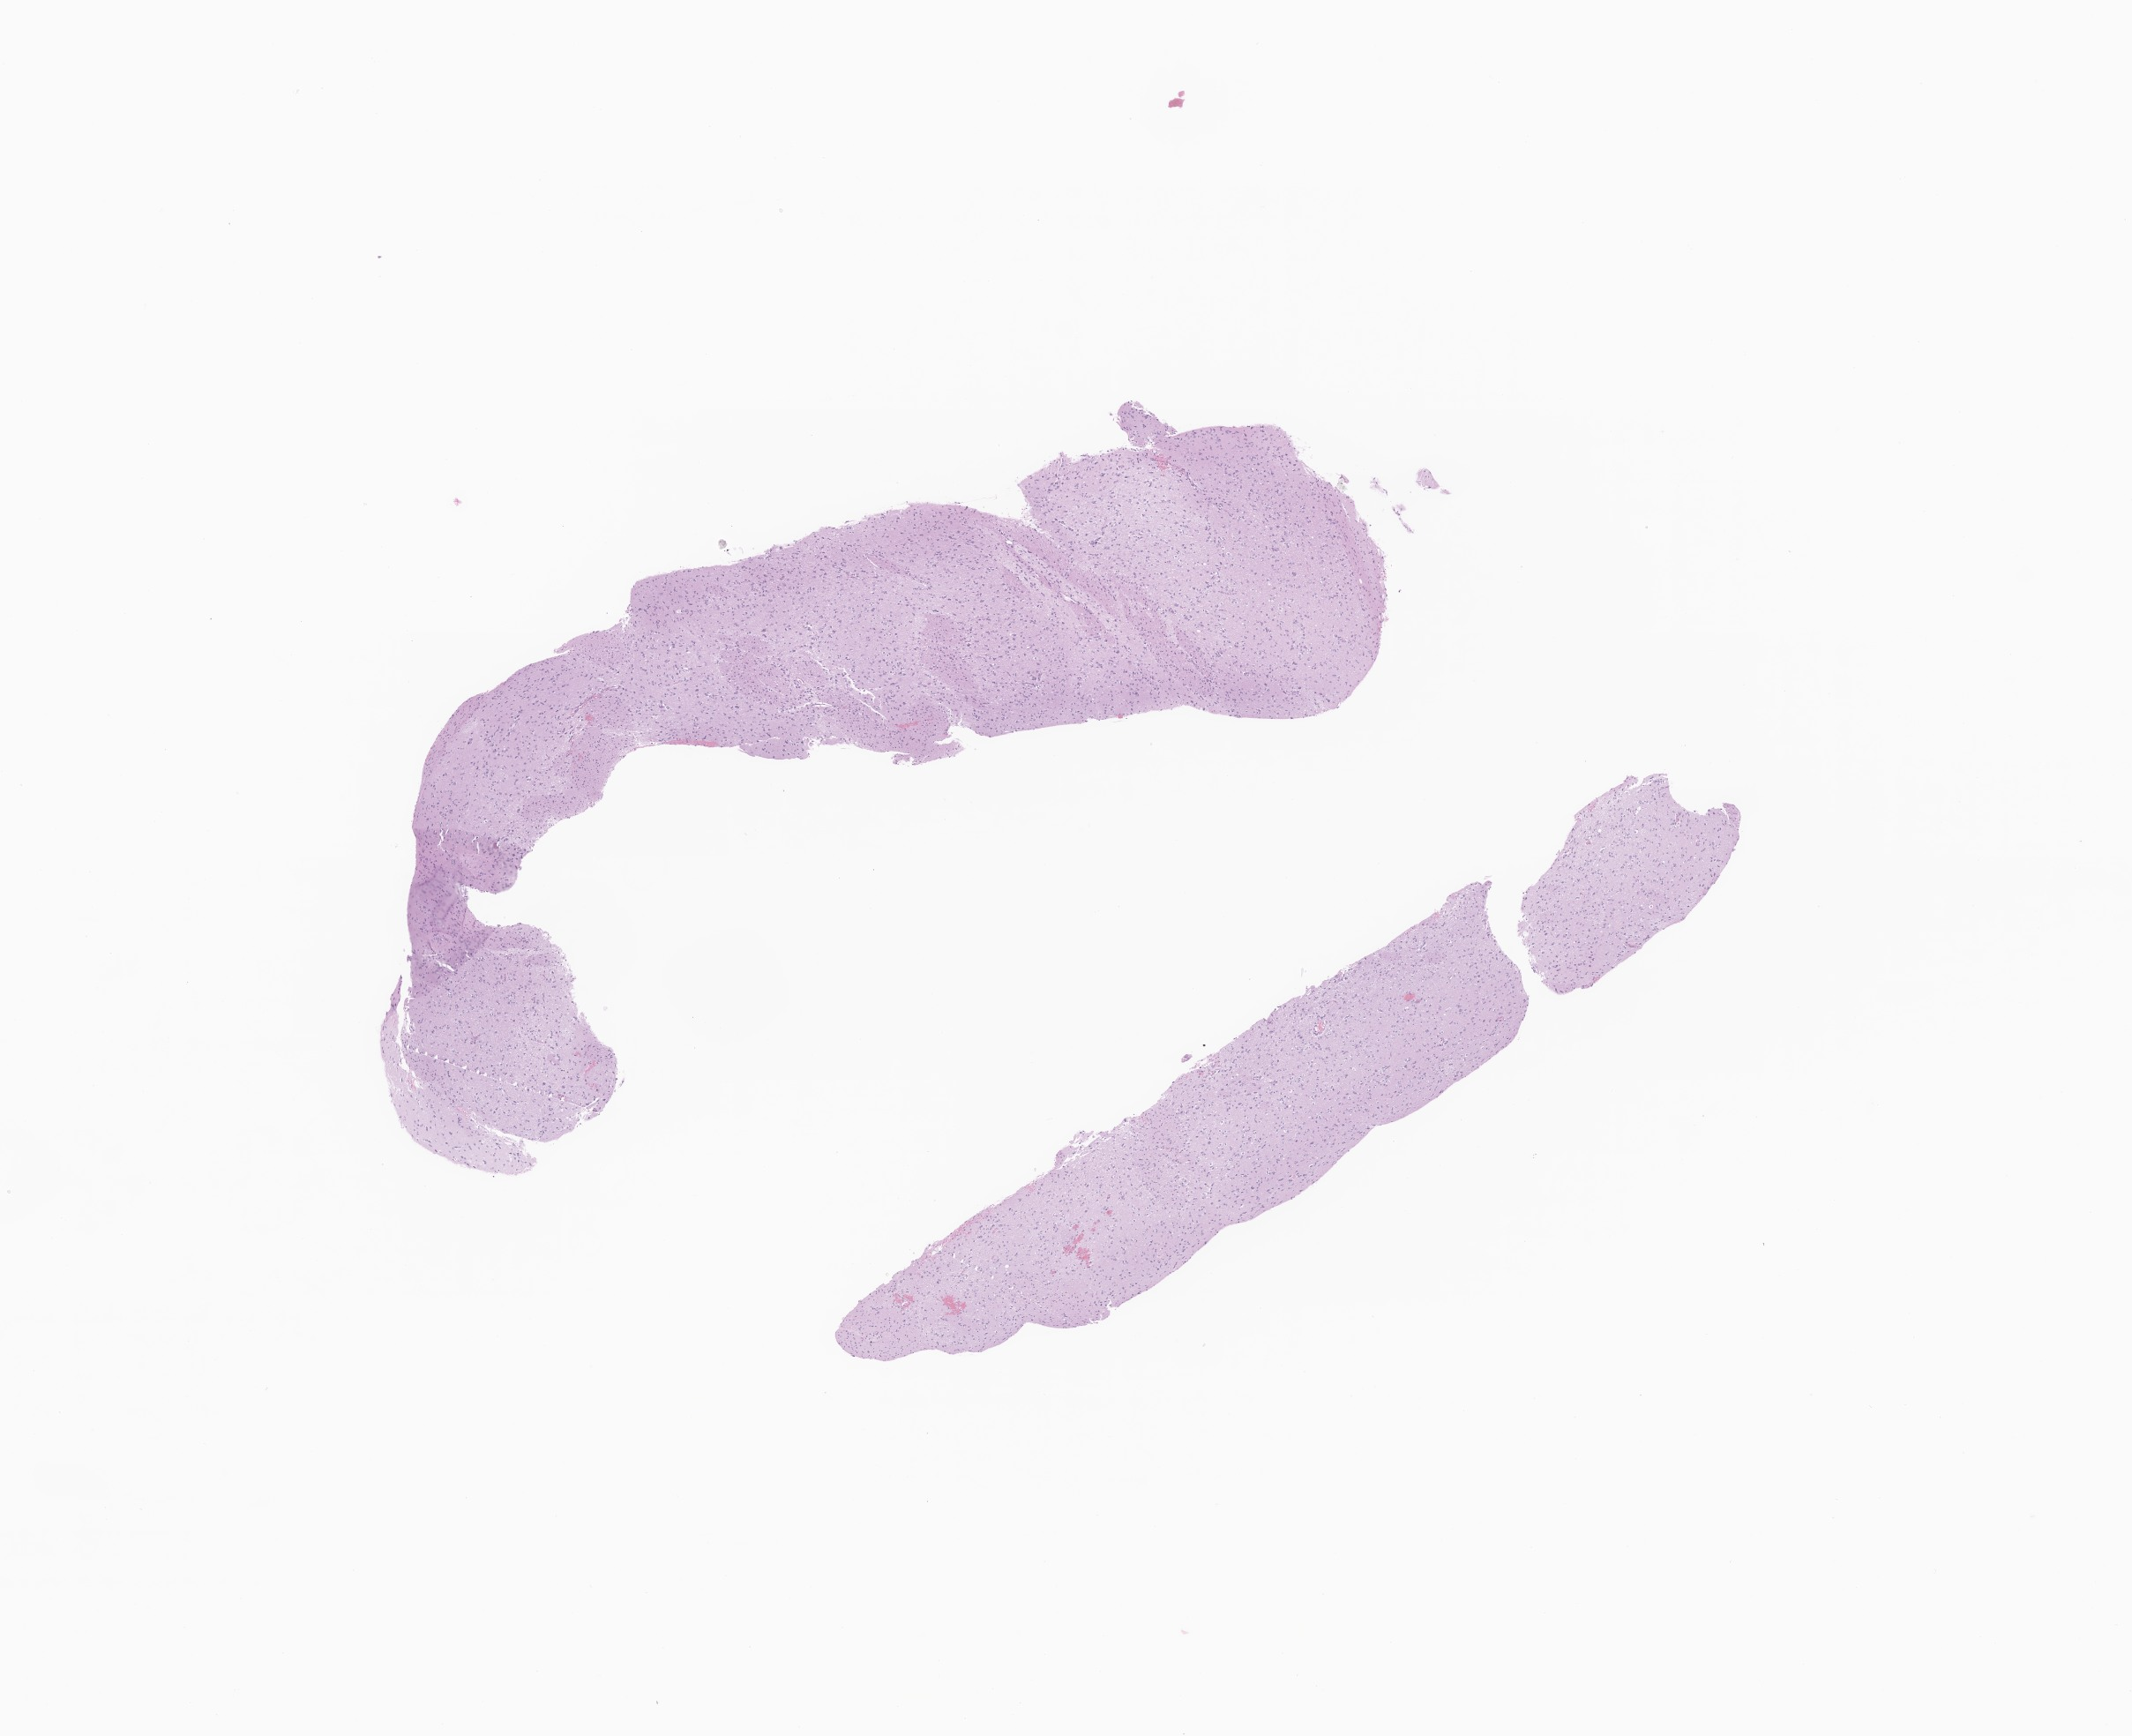
Whole-slide image, H&E stain of tumor tissue from the brain, whole scanned area (about 10.2 x 8.3 mm) shown as a low-resolution overview, formalin-fixed, paraffin-embedded (FFPE) tissue. Patient male; age 677 days (about 1.9 years).
Recorded diagnosis: Glioma, malignant.